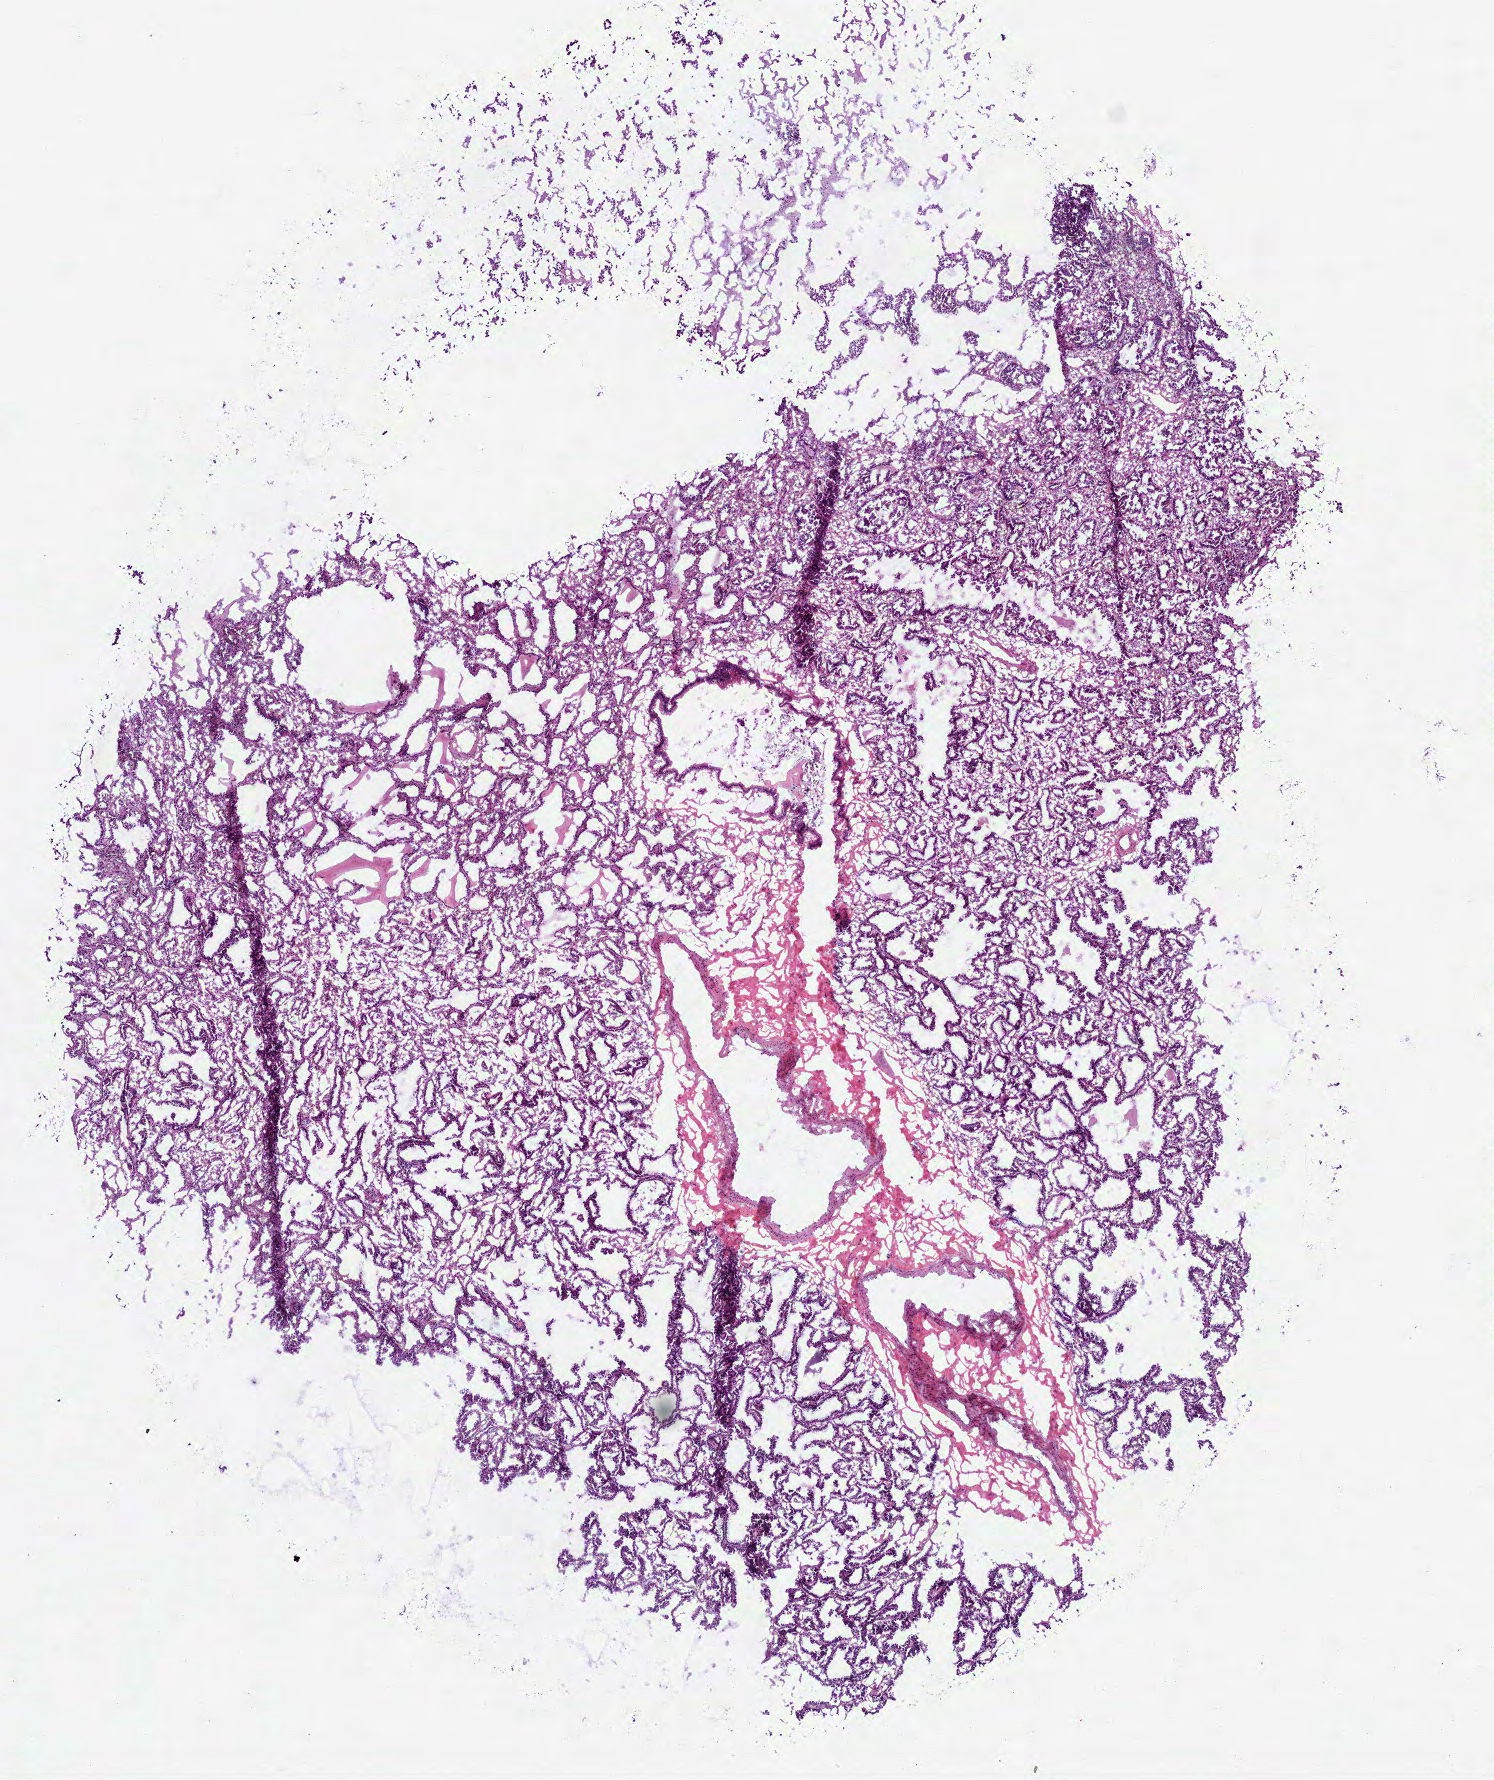
Digitized H&E tissue section (whole slide) — whole scanned area (about 6.0 x 7.2 mm) shown as a low-resolution overview. Frozen section. Primary tumour sample from the lung. Female patient; age at initial diagnosis 67 years. Pathologist review of this section (percent, as recorded): tumour cells 100%, tumour nuclei 80%, normal cells 0%, stromal cells 0%, necrosis 0%. Infiltration values recorded for this section: lymphocyte infiltration 5%, monocyte infiltration 0%, neutrophil infiltration 0%.
AJCC pathologic stage: IA. Histologic diagnosis: Adenocarcinoma, NOS (upper lobe, lung).